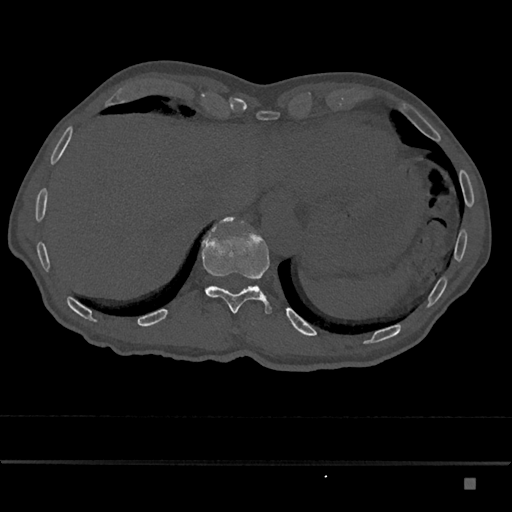
CT including the spine, one axial slice. Position 674 of 797 along the scan axis. 120 kVp. Bone window (W 1800 / L 400 HU). 0.5 mm slice thickness. 512 × 512 image matrix, field of view 390 × 390 mm. Male patient, age 72 years. Case-level facts recorded for this patient, not image findings: primary cancer: prostate.
Outlined on this slice (semi-automatically segmented with operator editing):
- T11 vertebra: bounding box [x1, y1, x2, y2] px = [201, 216, 272, 314]